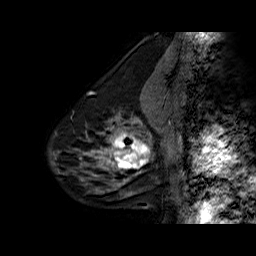
Breast MRI (dynamic contrast-enhanced), one sagittal slice. Slice 20 of 60 in the series (ordered by position). Dynamic contrast-enhanced series, time point 2 of 6 at this slice position (early post-contrast). 1.5 T. TE 6.3 ms, TR 32.5 ms. 4 mm slice thickness. 256 × 256 image matrix. Female patient. Case-level facts recorded for this patient, not image findings: setting: breast cancer imaged before/during neoadjuvant chemotherapy; receptor status: triple-negative.
Structures marked on this image (semi-automatically segmented with operator editing):
- analysis volume of interest (the breast-tissue region the enhancement analysis was run in; not a lesion): bounding box [x1, y1, x2, y2] px = [108, 126, 154, 177]
- tumour enhancement mask (voxels above the 100 % enhancement threshold inside the analysis volume of interest): [108, 131, 150, 174]